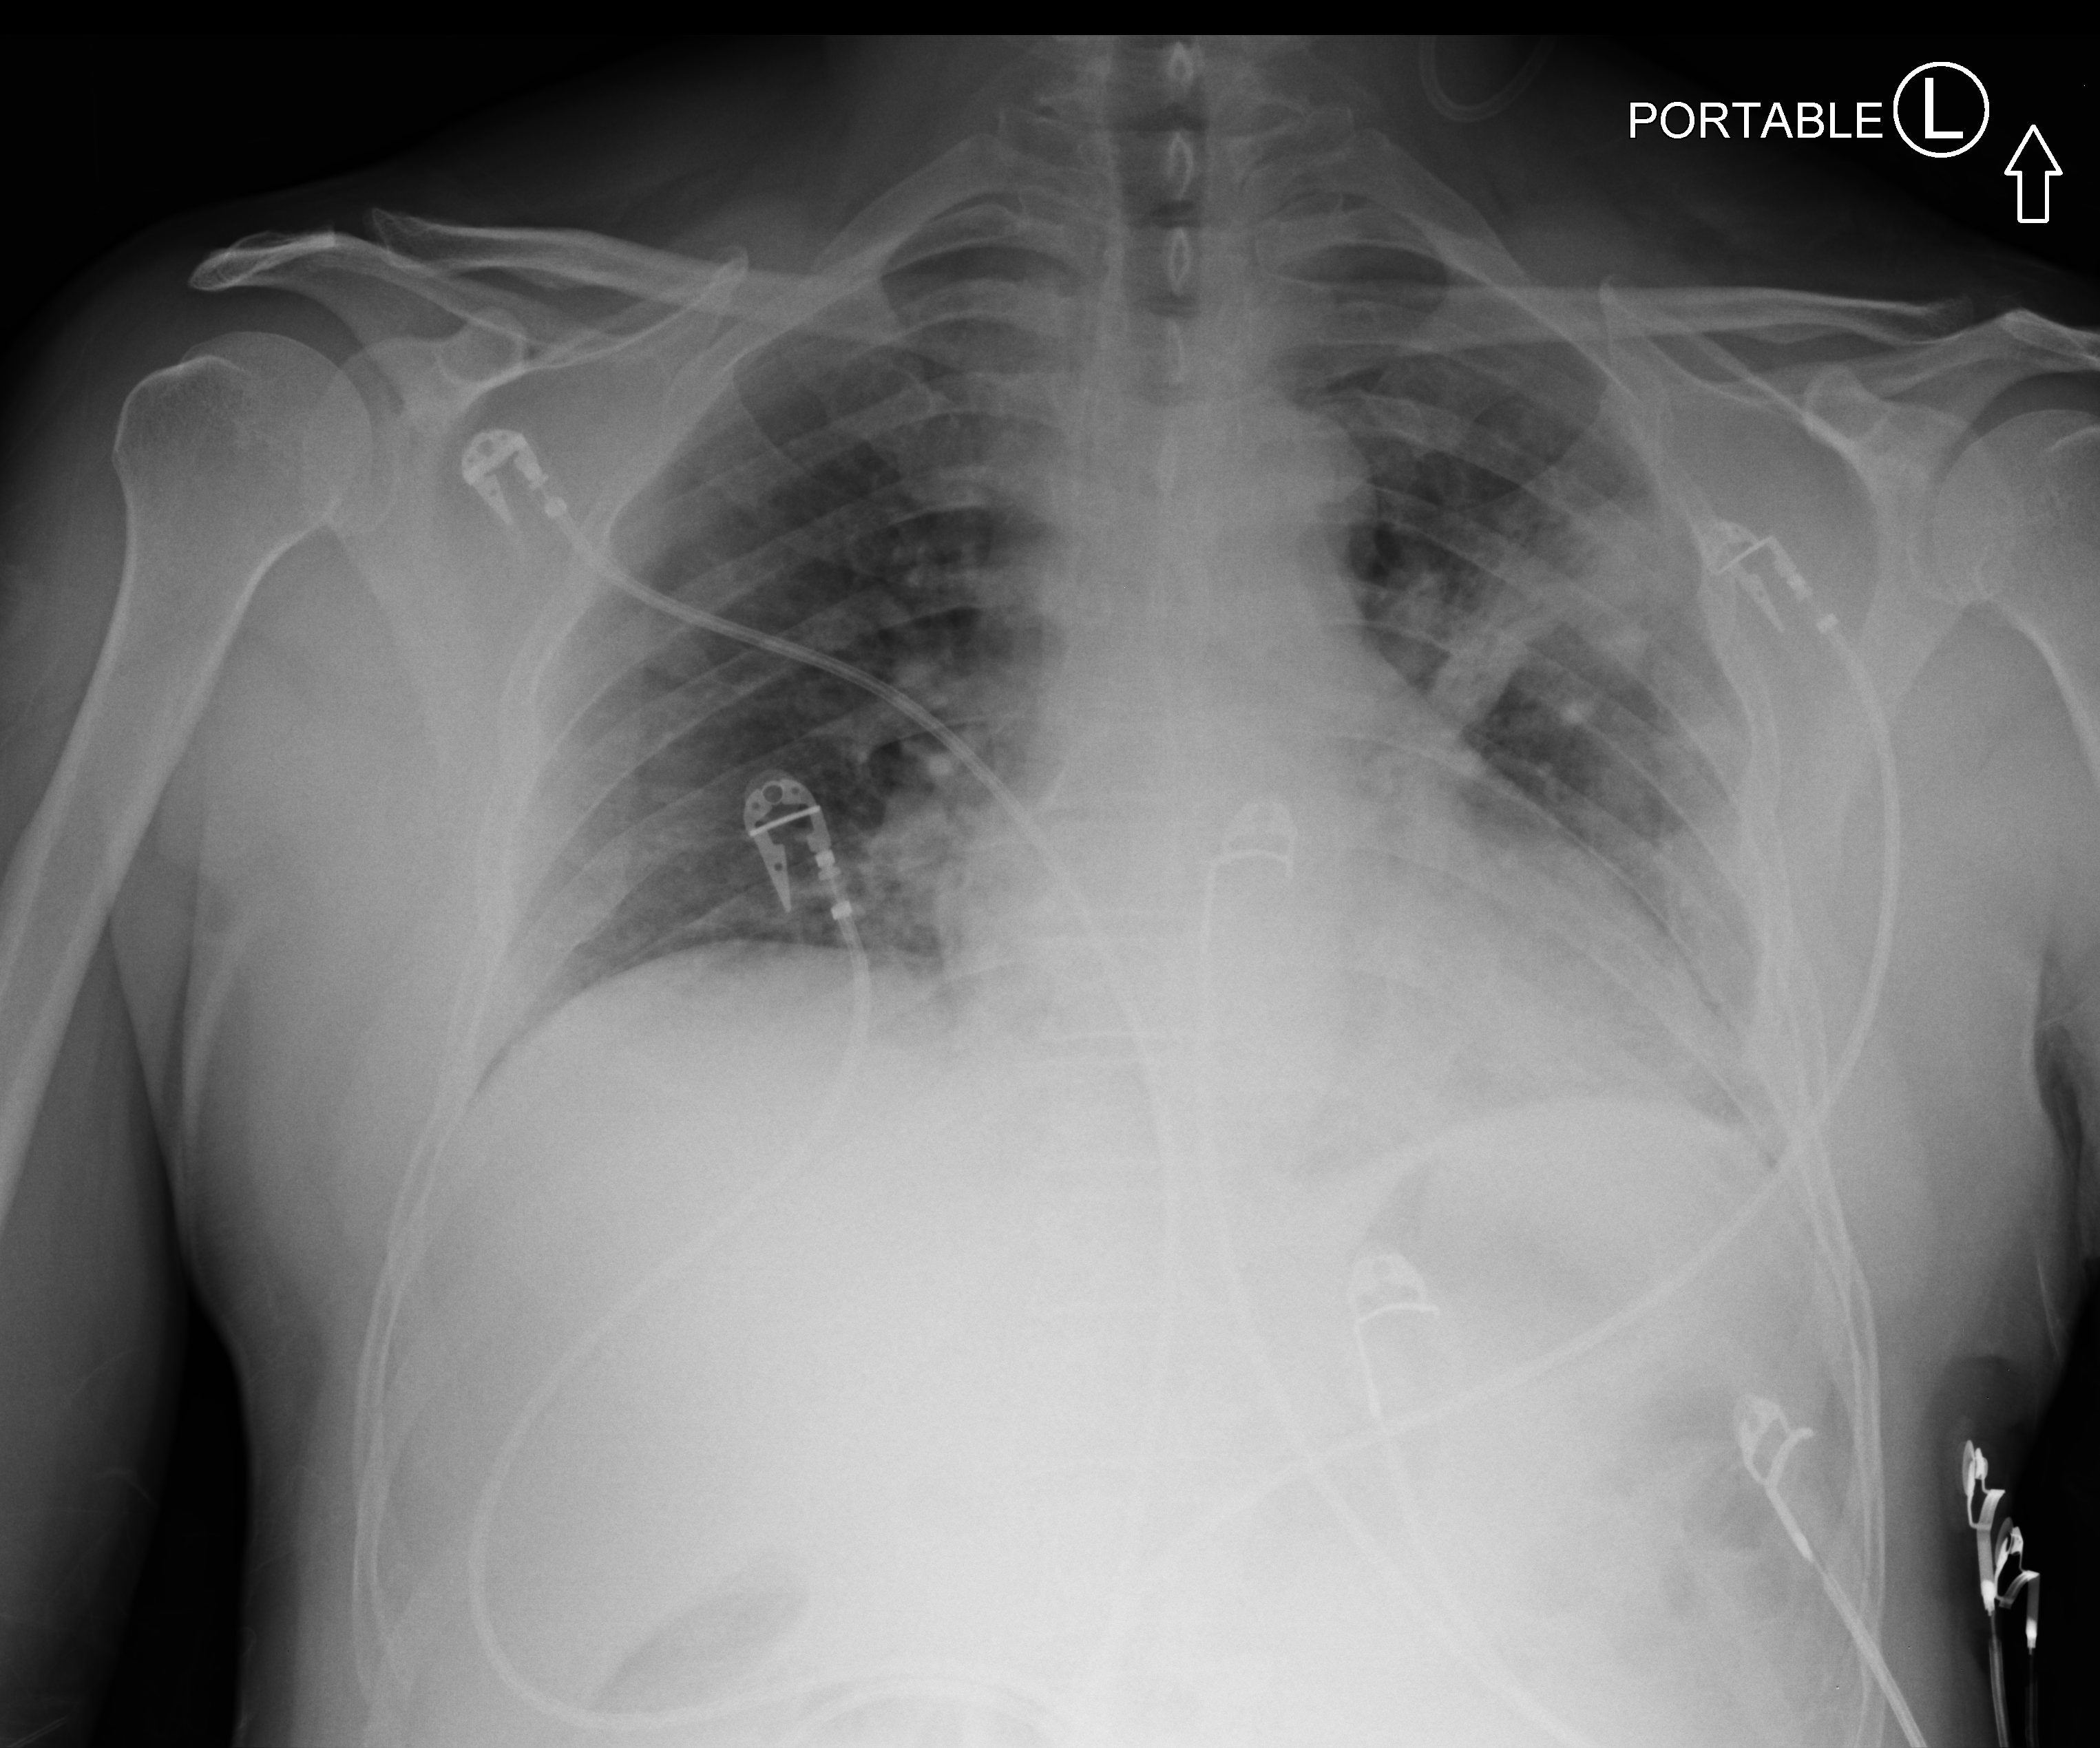
Portable chest radiograph. Patient hospitalised with COVID-19; male, aged 18–59 years.
From the hospital-stay record, not from the radiograph (when in the stay this image was taken is not recorded): length of hospital stay: 14 days; mechanically ventilated during this hospital stay: yes.